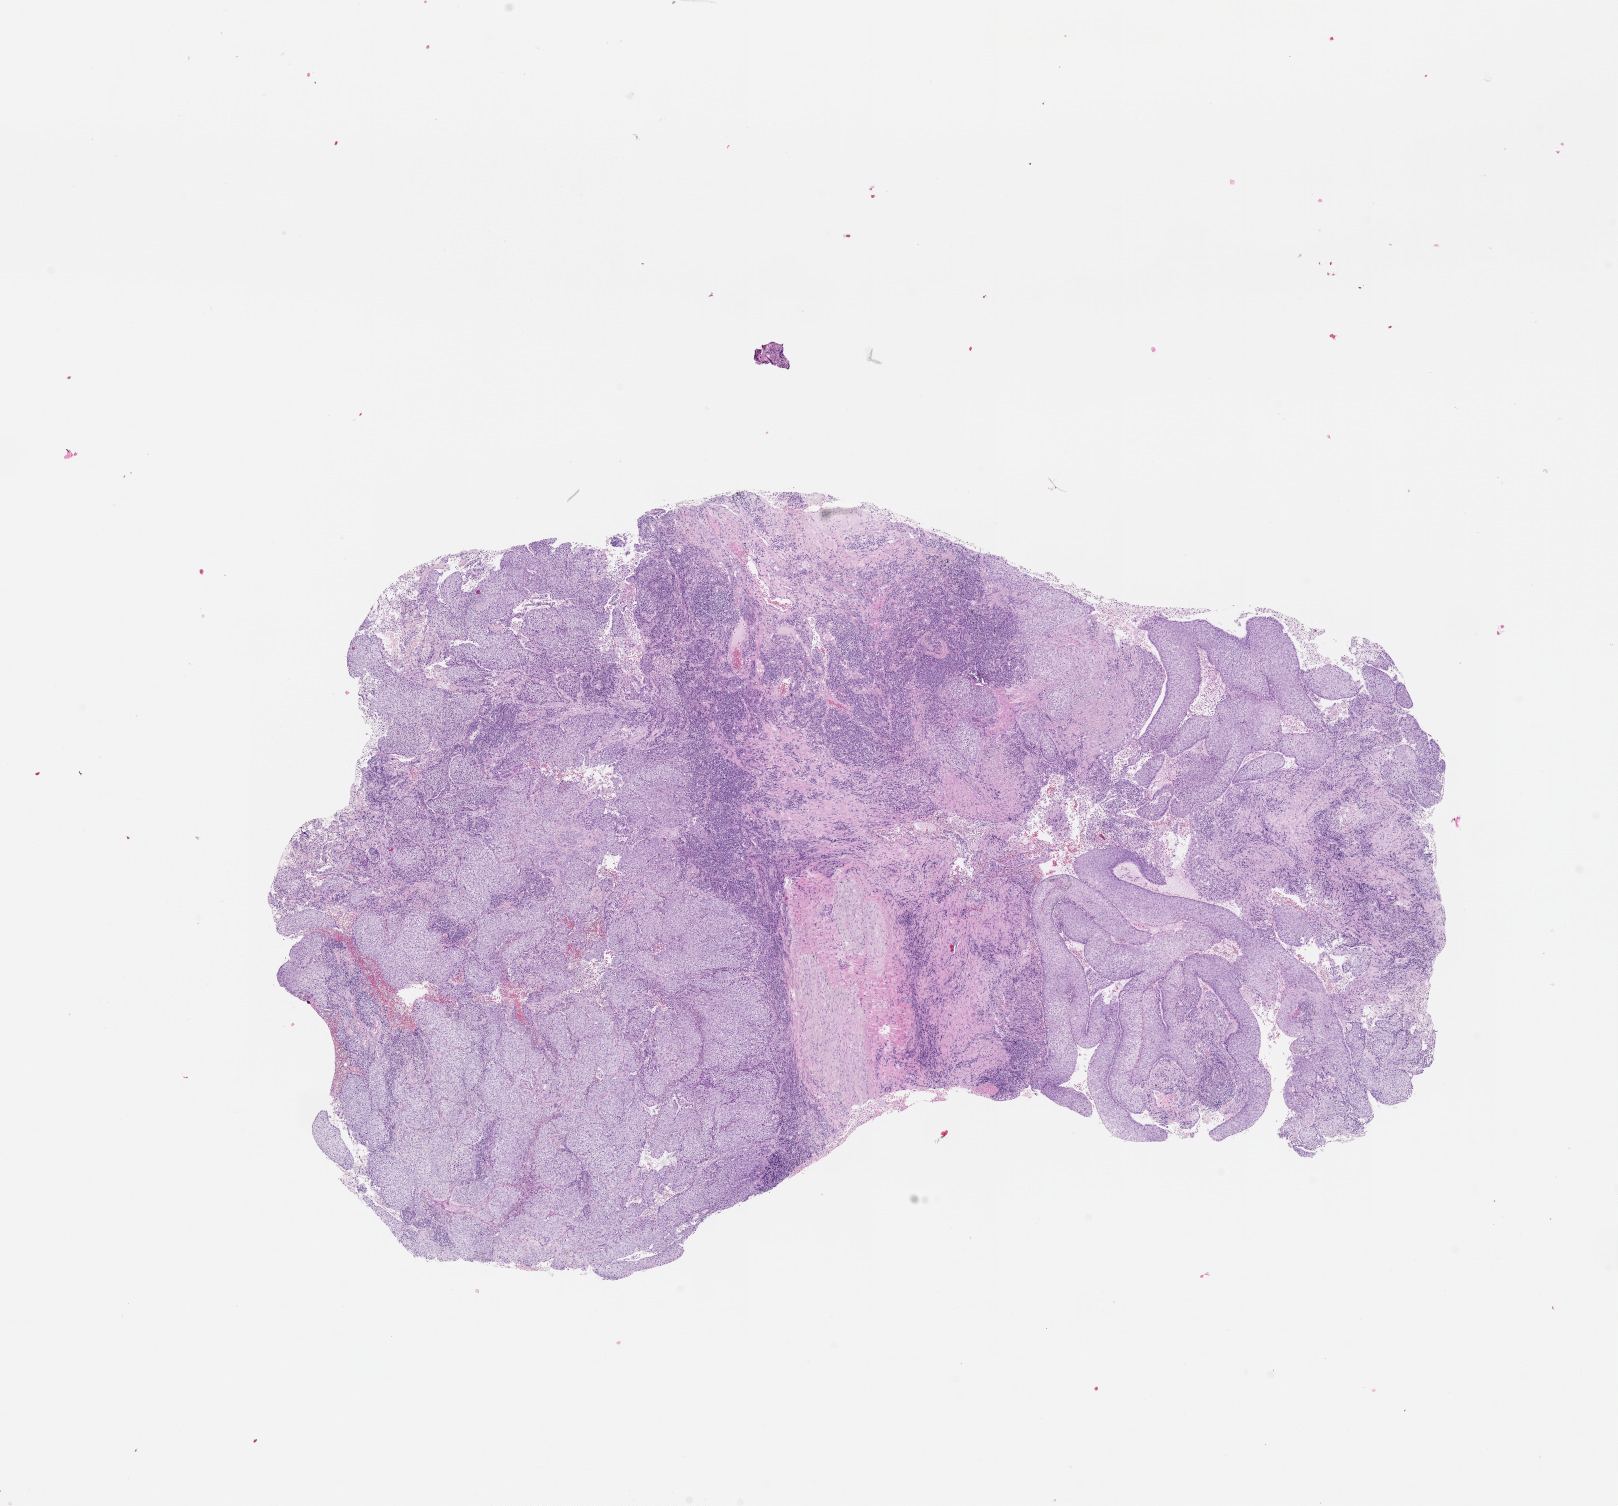
Digitized H&E-stained tissue section (whole slide), whole scanned area (about 13.0 x 12.1 mm) shown as a low-resolution overview, lung, tumour tissue. Male, 60 y/o.
Patient diagnosis (cohort enrolment): squamous cell carcinoma (lung).